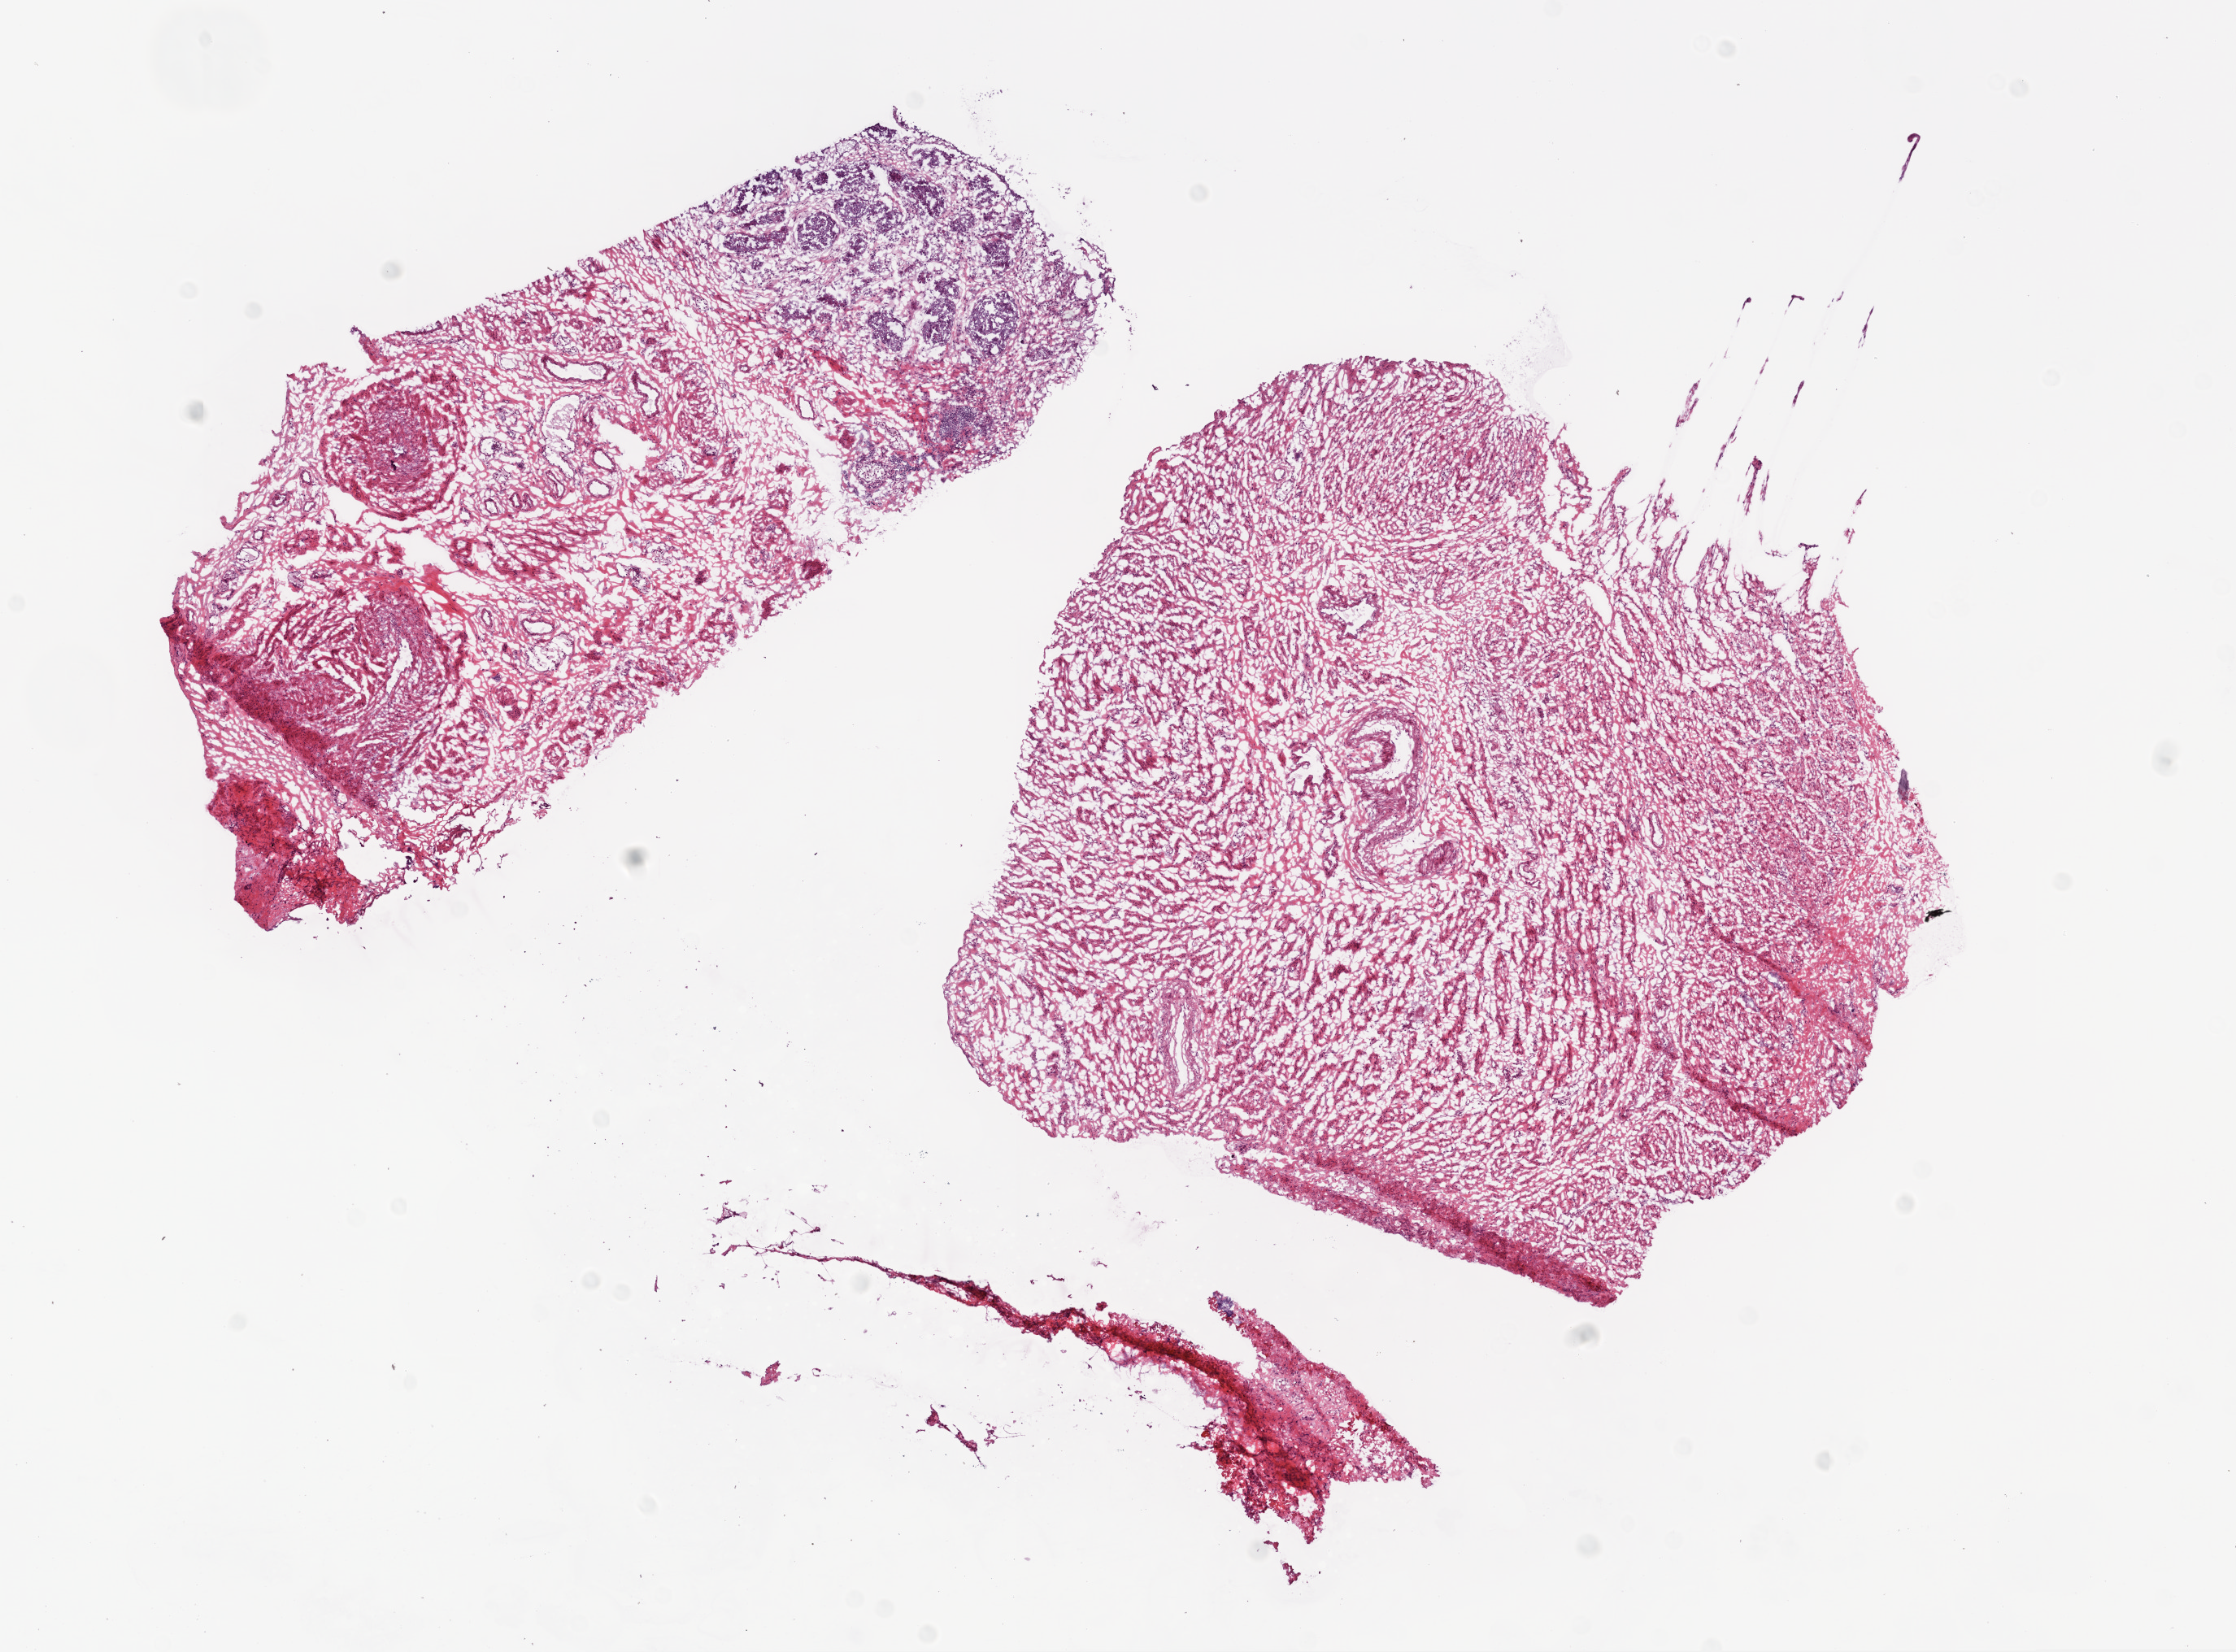
Whole-slide histology image, H&E-stained, whole scanned area (about 11.0 x 8.2 mm) shown as a low-resolution overview, frozen section from the bottom of the tissue portion, primary tumour sample from the ovary. Female patient; age at initial diagnosis 65 years. Pathologist review of this section (percent, as recorded): tumour cells 10%, tumour nuclei 90%.
Diagnosis: Serous cystadenocarcinoma, NOS.